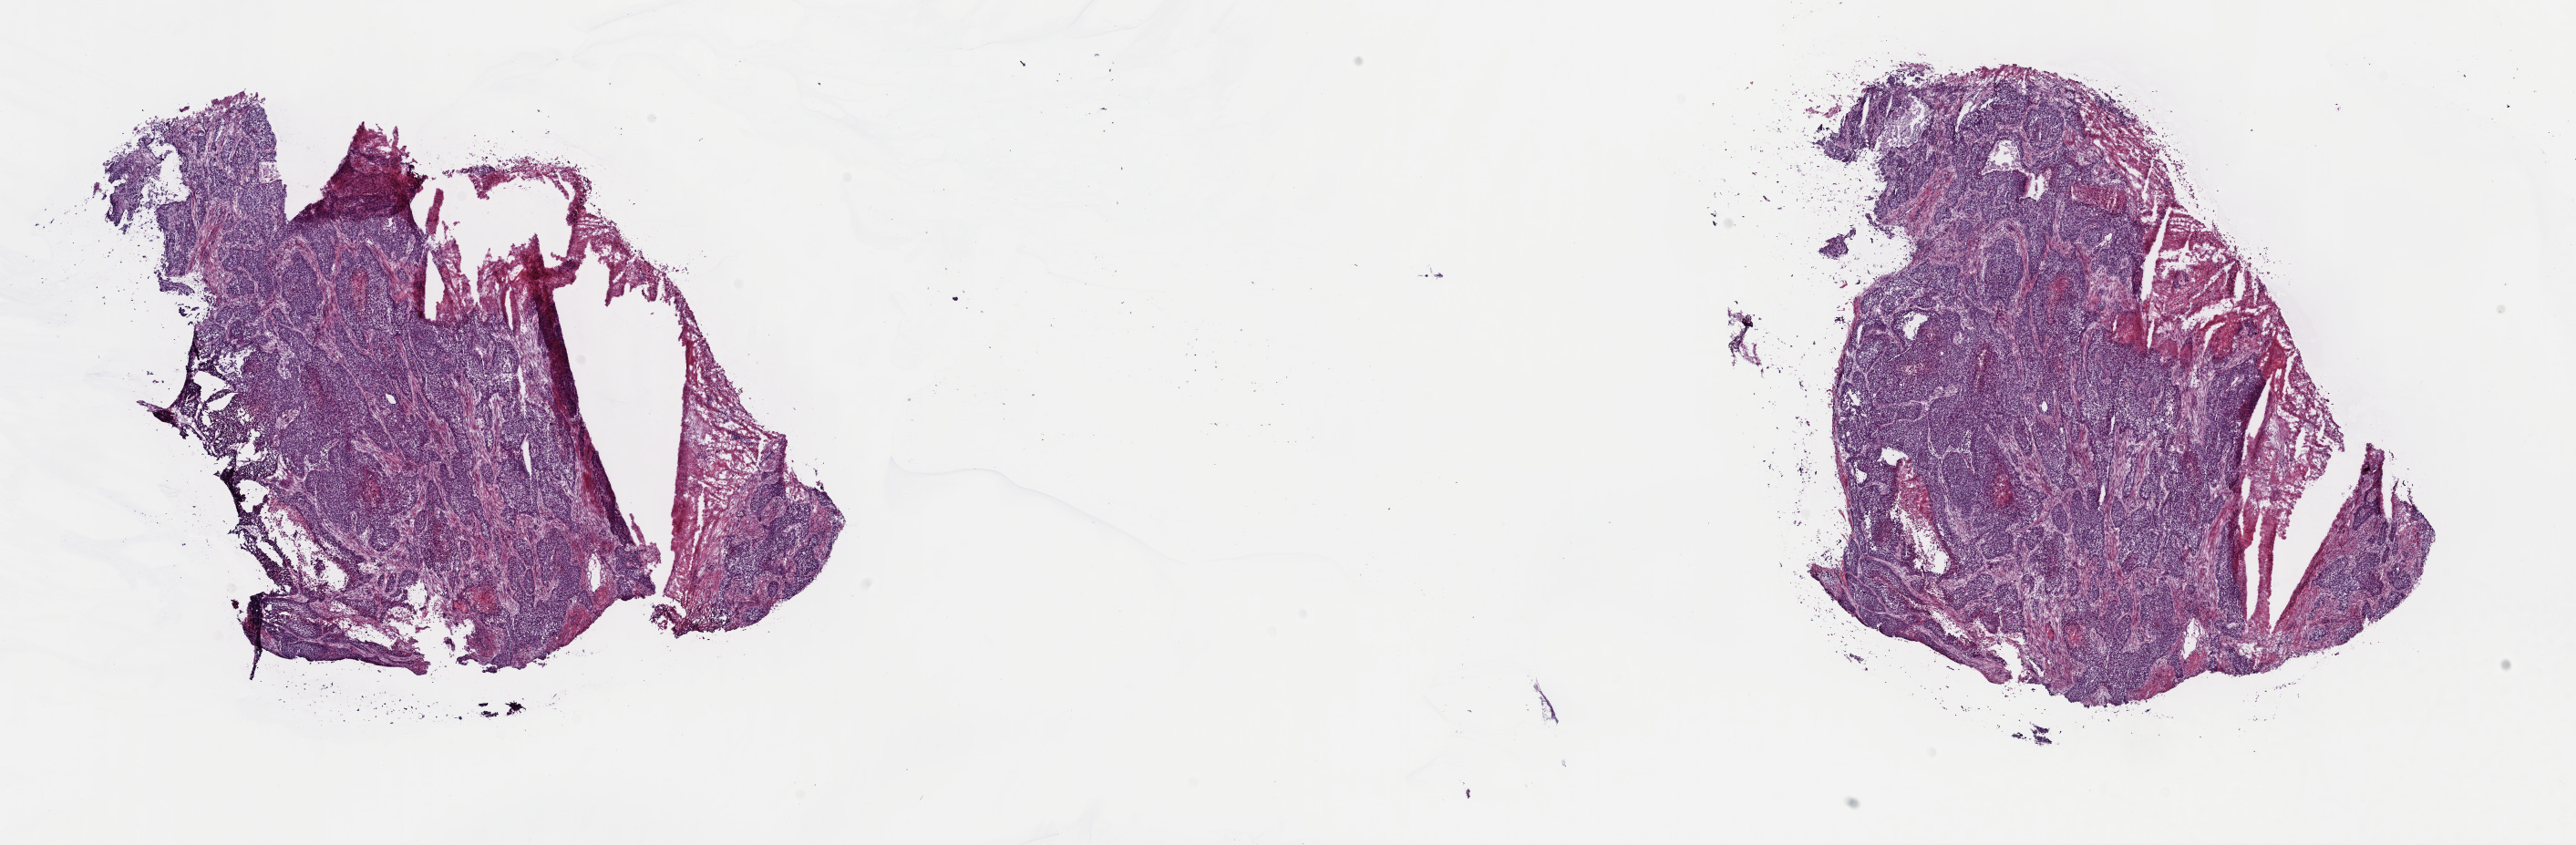
H&E-stained whole-slide image, low-resolution overview of the scanned area, about 22.3 x 7.3 mm (slide scanned at 40x). Frozen section from the top of the tissue portion. Lung, primary tumour sample. Male patient; age at initial diagnosis 68 years. Slide review estimates, as recorded: tumour cells 45%, tumour nuclei 100%, normal cells 0%, stromal cells 35%, necrosis 20%. Infiltration values recorded for this section: lymphocyte infiltration 2%, monocyte infiltration 1%, neutrophil infiltration 0%.
- laterality: right
- AJCC pathologic stage: IB
- histologic diagnosis: Squamous cell carcinoma, NOS (lower lobe, lung)